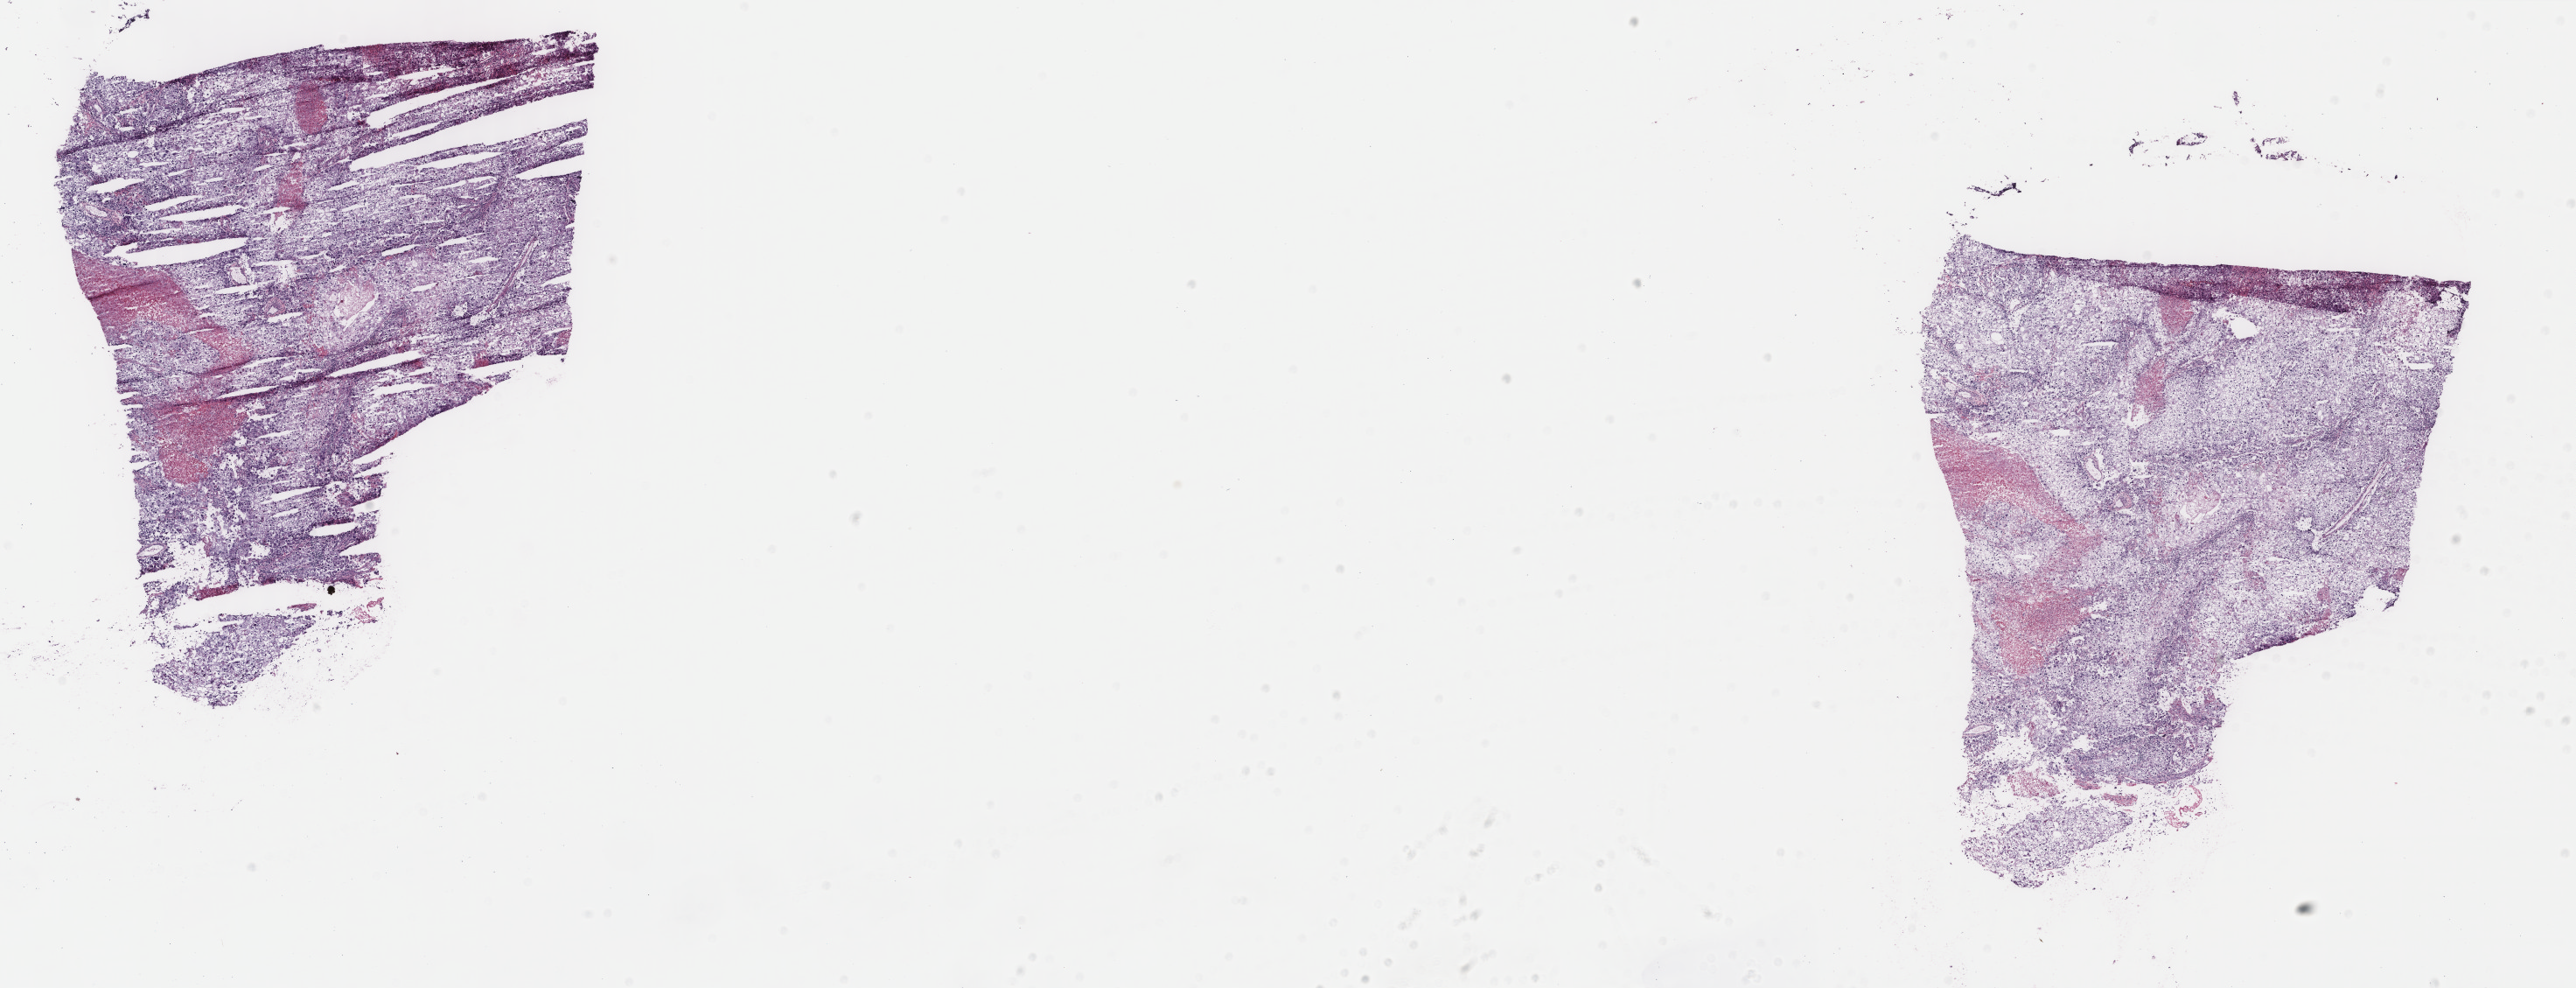
H&E-stained whole-slide image — whole scanned area (about 23.4 x 9.0 mm) shown as a low-resolution overview, frozen section from the top of the tissue portion, primary tumour sample from the cervix. Female patient; age at initial diagnosis 51 years. Histologic grade: G3 (poorly differentiated). Composition of this section per pathologist review: tumour cells 86%, tumour nuclei 70%, normal cells 0%, stromal cells 2%, necrosis 12%. Inflammatory infiltration, as recorded: lymphocyte infiltration 20%, monocyte infiltration 0%, neutrophil infiltration 5%.
Pathologic diagnosis: Squamous cell carcinoma, NOS (cervix uteri). FIGO stage: IB2.